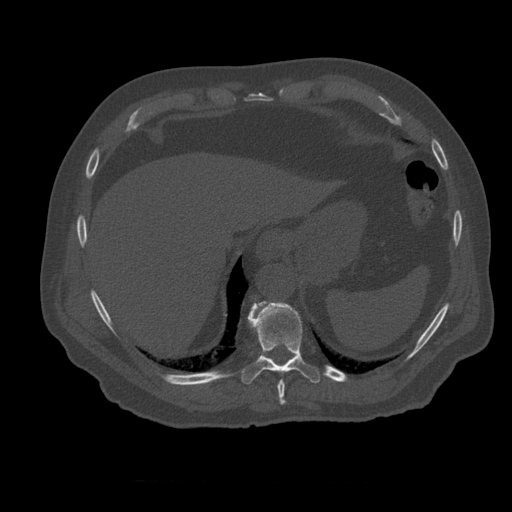
CT including the spine, one axial slice. Slice 303 of 399 in the series (ordered by position). Reconstruction kernel STANDARD. 120 kVp. Bone window (W 1800 / L 400 HU). 512 × 512 image matrix, field of view 407 × 407 mm. Patient age 73 years. Case-level facts recorded for this patient, not image findings: primary cancer: prostate; vertebrae with lytic lesions (as recorded): L2.
Annotated regions visible in this slice (semi-automatic segmentation, software-assisted and operator-edited):
- T10 vertebra: bounding box (x1, y1, x2, y2) in pixels: (241, 302, 321, 385)
- T11 vertebra: (263, 354, 274, 362)
- T9 vertebra: (278, 372, 286, 405)